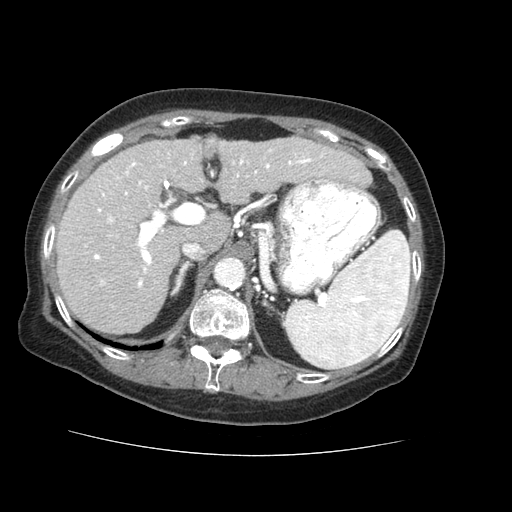
Contrast-enhanced abdominal CT (liver protocol), one axial slice. Slice 39 of 73 in the series (ordered by position). 120 kVp. Soft-tissue window (W 400 / L 40 HU). 2.5 mm slice thickness. 512 × 512 image matrix. From the clinical record (not read from this slice): diagnosis: hepatocellular carcinoma (patient treated with transarterial chemoembolisation; whether this scan precedes or follows treatment is not stated here); TNM stage (as recorded): Stage-IVB; Child-Pugh class: A.
Outlined on this slice (semi-automatic segmentation, software-assisted and operator-edited):
- liver parenchyma outside the tumour (the mass and vessels are separate outlines, so this box may not span the whole liver): bounding box (x1, y1, x2, y2) in pixels: (54, 138, 372, 334)
- mass: (204, 139, 217, 155)
- liver vessels: (85, 149, 324, 288)